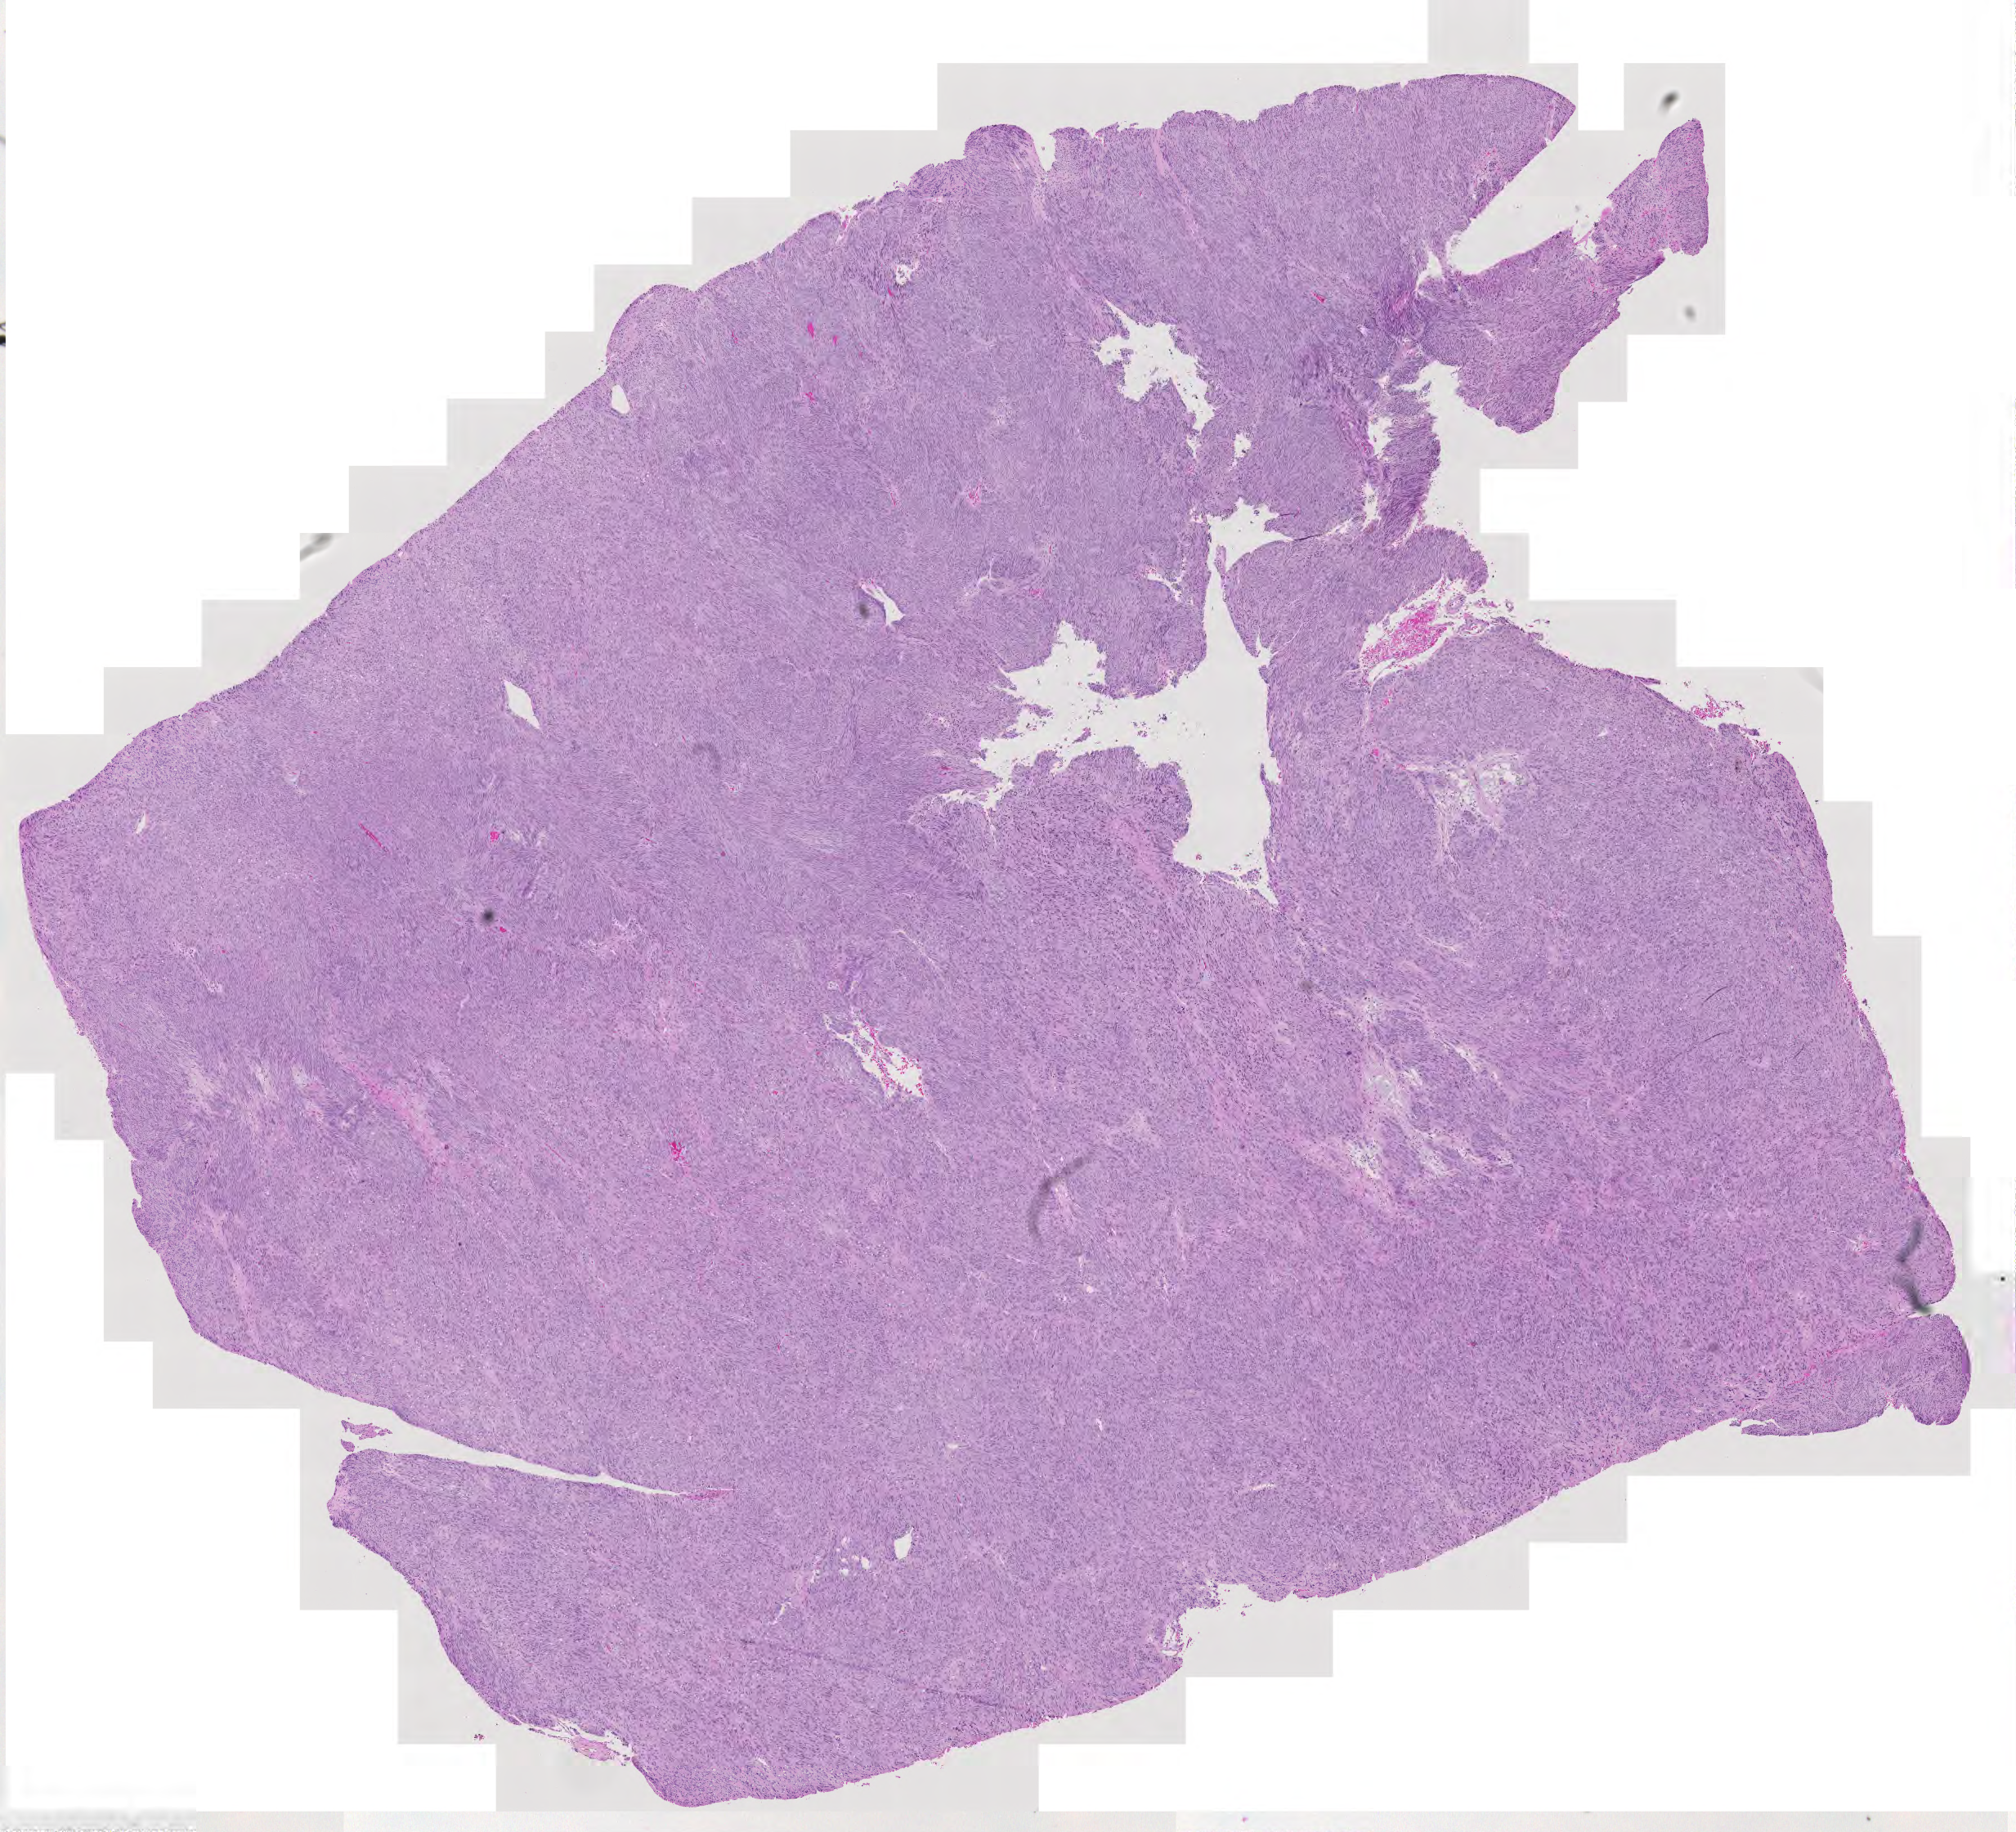
H&E-stained whole-slide image, a low-resolution overview of the entire scanned area, about 12.7 x 11.6 mm. Patient: male, age 87 years.
Patient diagnosis (cohort enrolment): sarcoma (site not recorded at cohort level).